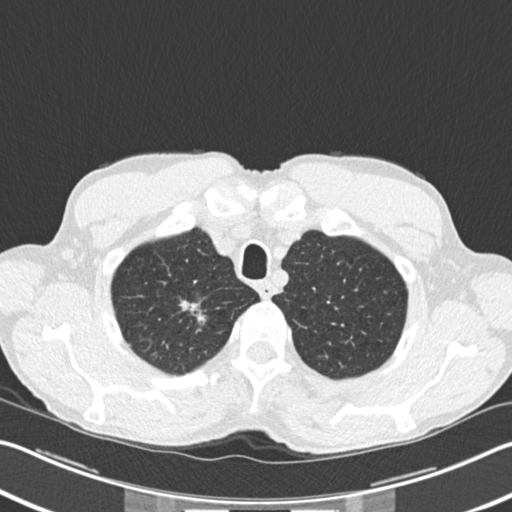
Low-dose screening chest CT, one axial slice; position 191 of 220 along the scan axis; 120 kVp; lung window (W 1500 / L -600 HU); 2 mm slice thickness; 512 × 512 image matrix, field of view 342 × 342 mm.
Outlined on this slice (manually delineated by an expert):
- lesion 1 (tumor, upper lobe of right lung): box from (x=180, y=300) to (x=206, y=323) px